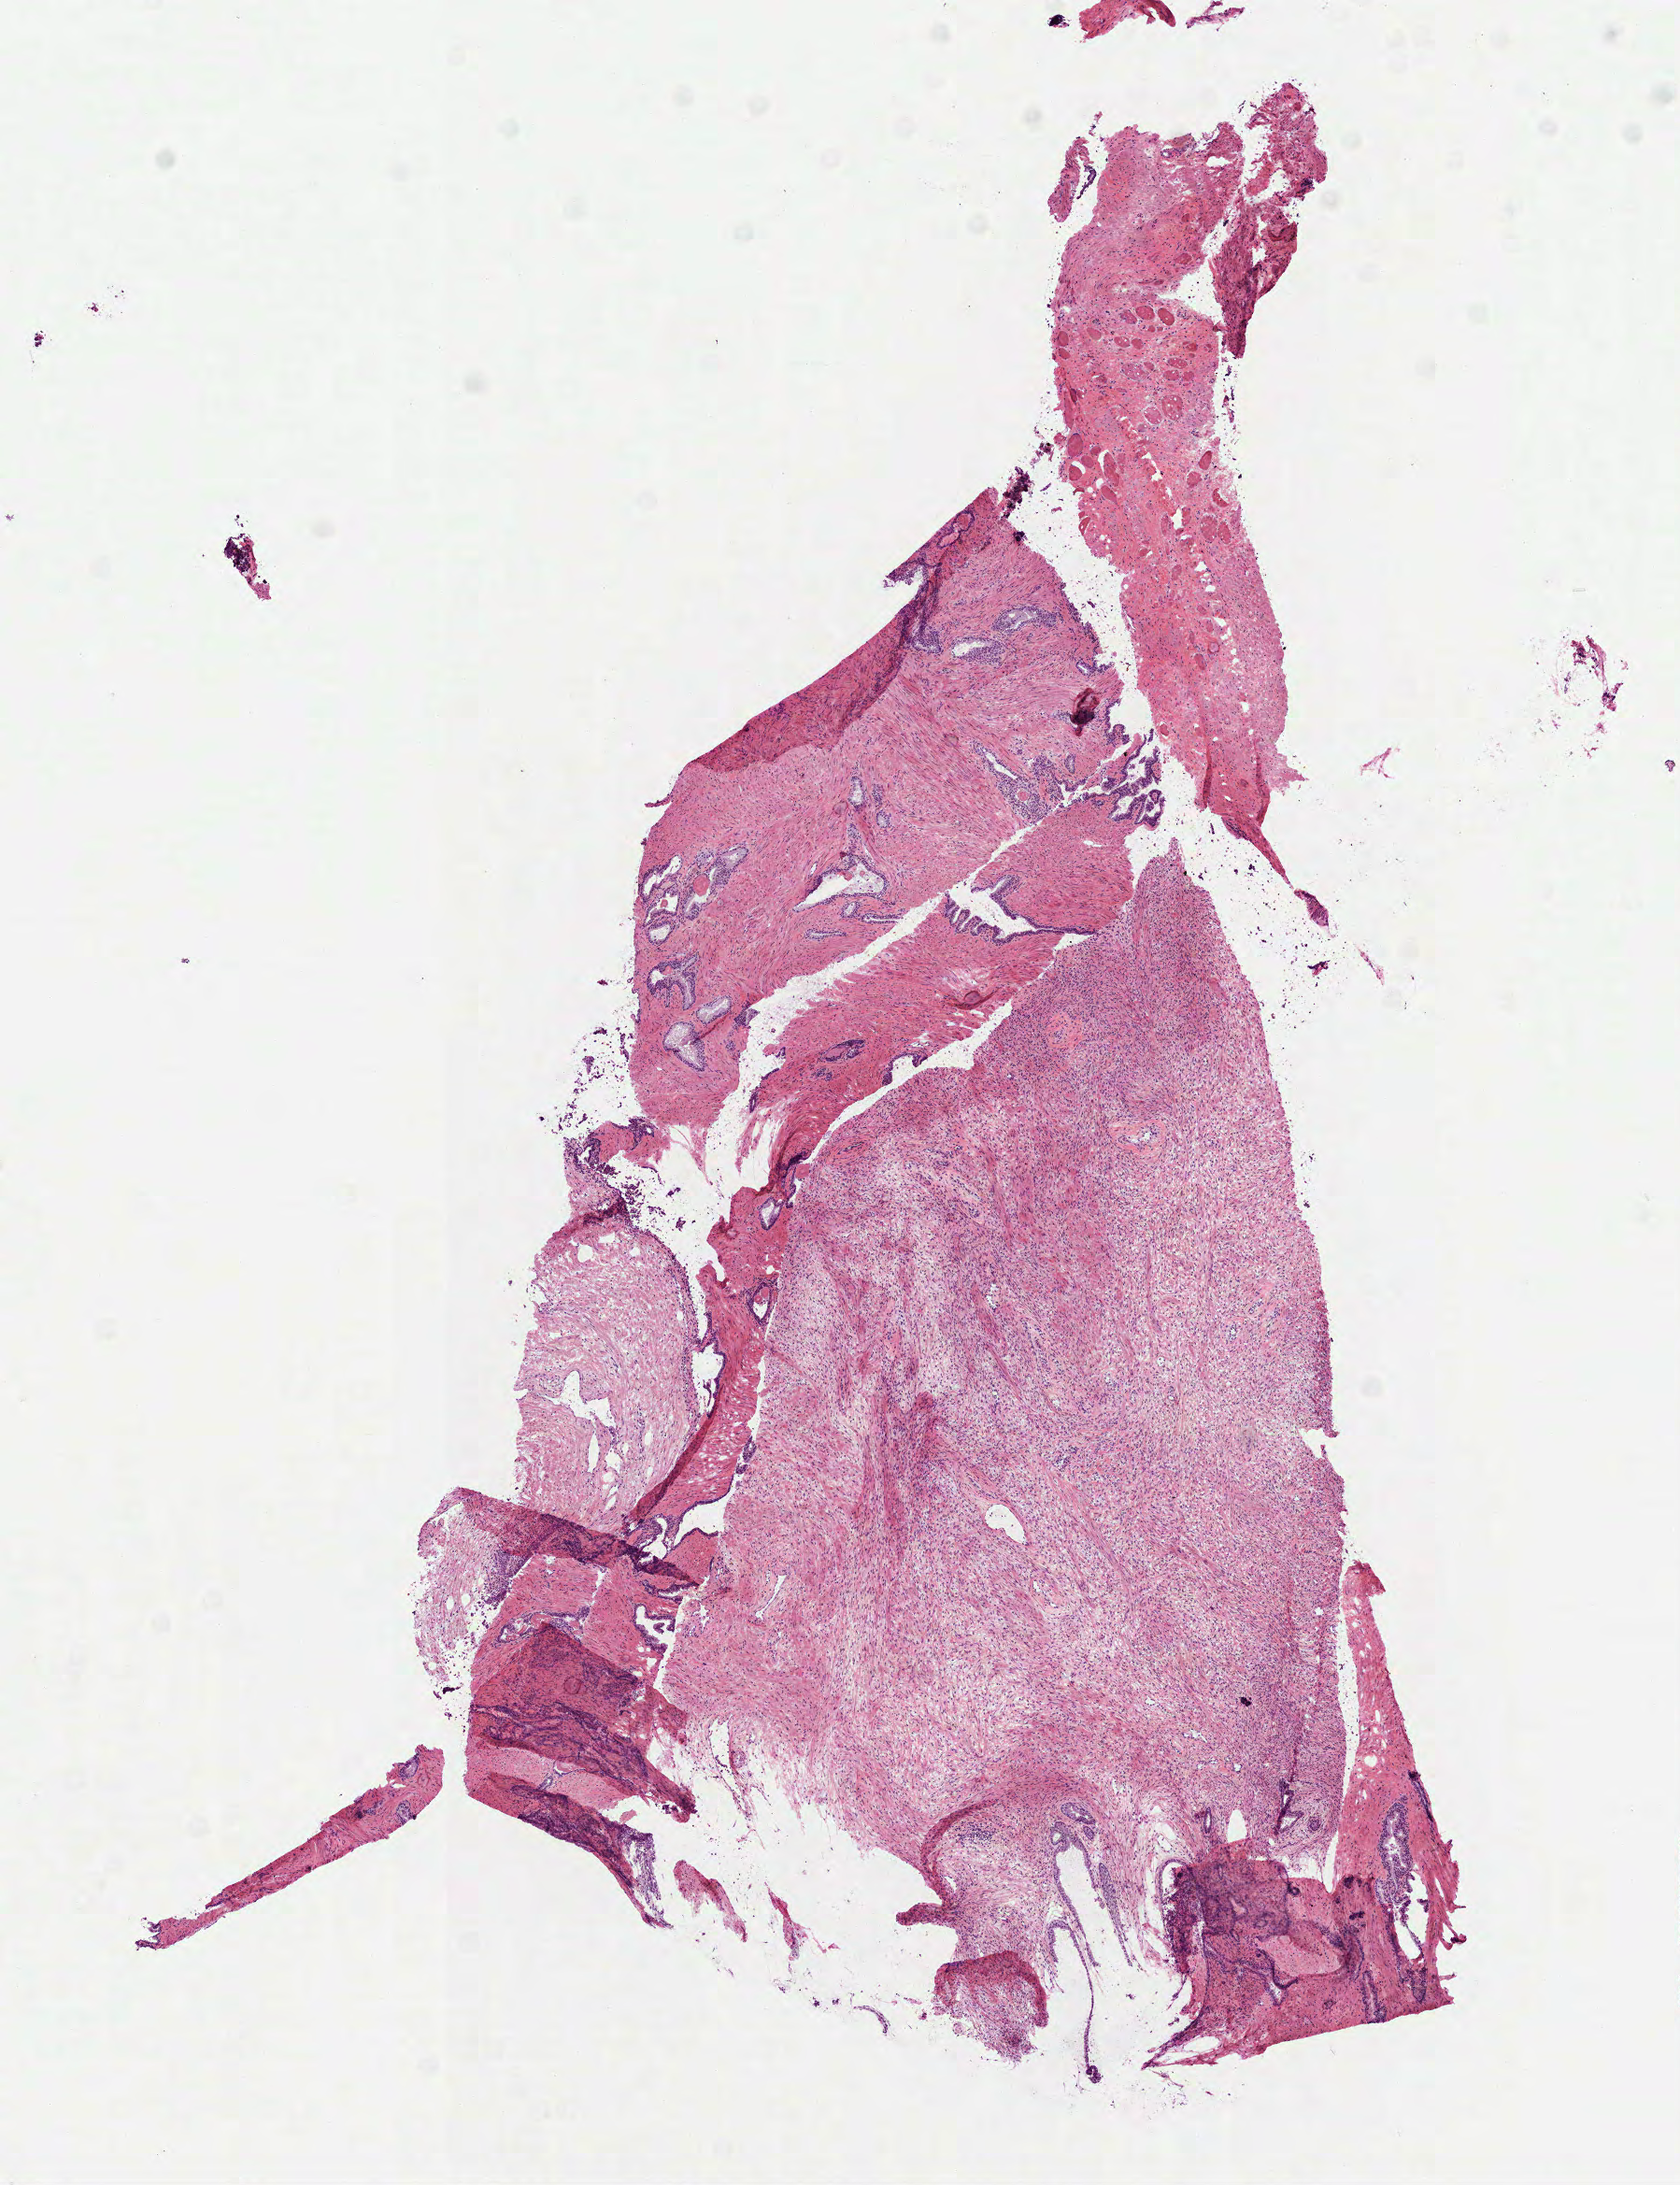
H&E whole-slide image, low-resolution overview of the scanned area, about 7.3 x 9.4 mm, frozen section from the top of the tissue portion, prostate, solid tissue normal (non-tumour tissue) sample. Male patient; age at initial diagnosis 64 years.
• this section: solid tissue normal sample (biorepository sample class)
• patient diagnosis: Acinar cell carcinoma (prostate gland)